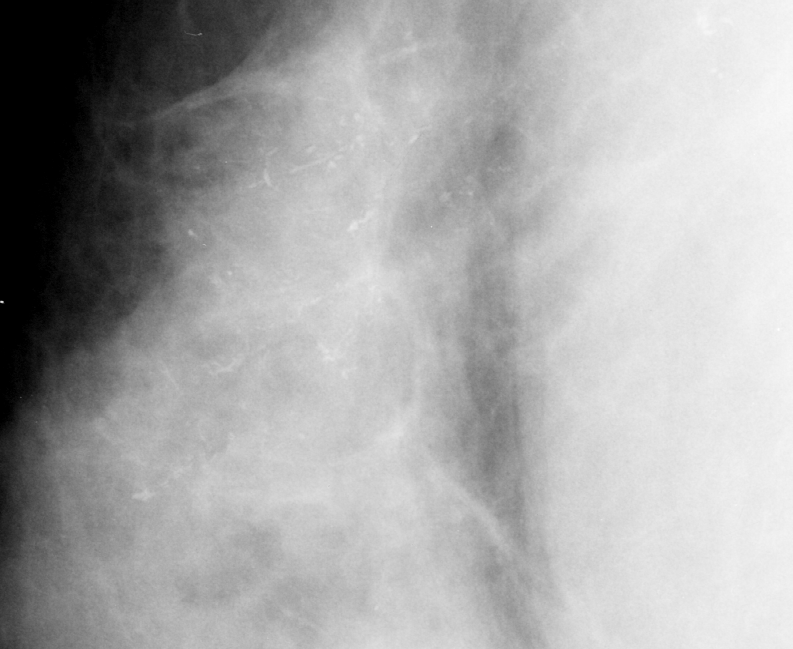
Cropped region of a digitized screen-film mammogram centred on a radiologist-marked abnormality, right breast, CC view, BI-RADS breast density category 3 (scale 1–4).
Calcifications, morphology fine linear branching, distribution linear / segmental; BI-RADS assessment category 5; subtlety rating 3 on a 1 (subtle) to 5 (obvious) scale; pathology result (as recorded, not read from the image): malignant.